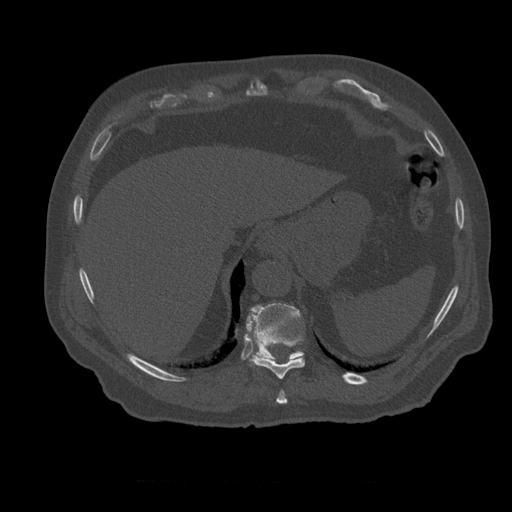
CT including the spine, one axial slice; position 296 of 399 along the scan axis; reconstruction kernel STANDARD; 120 kVp; bone window (W 1800 / L 400 HU); 1.25 mm slice thickness; 512 × 512 image matrix, field of view 407 × 407 mm. Patient age 73 years. From the clinical record (not read from this slice): primary cancer: prostate.
Structures marked on this image (semi-automatic segmentation, software-assisted and operator-edited):
- T10 vertebra: bounding box [x1, y1, x2, y2] px = [250, 336, 305, 380]
- T11 vertebra: [246, 303, 304, 361]
- T9 vertebra: [276, 391, 288, 405]